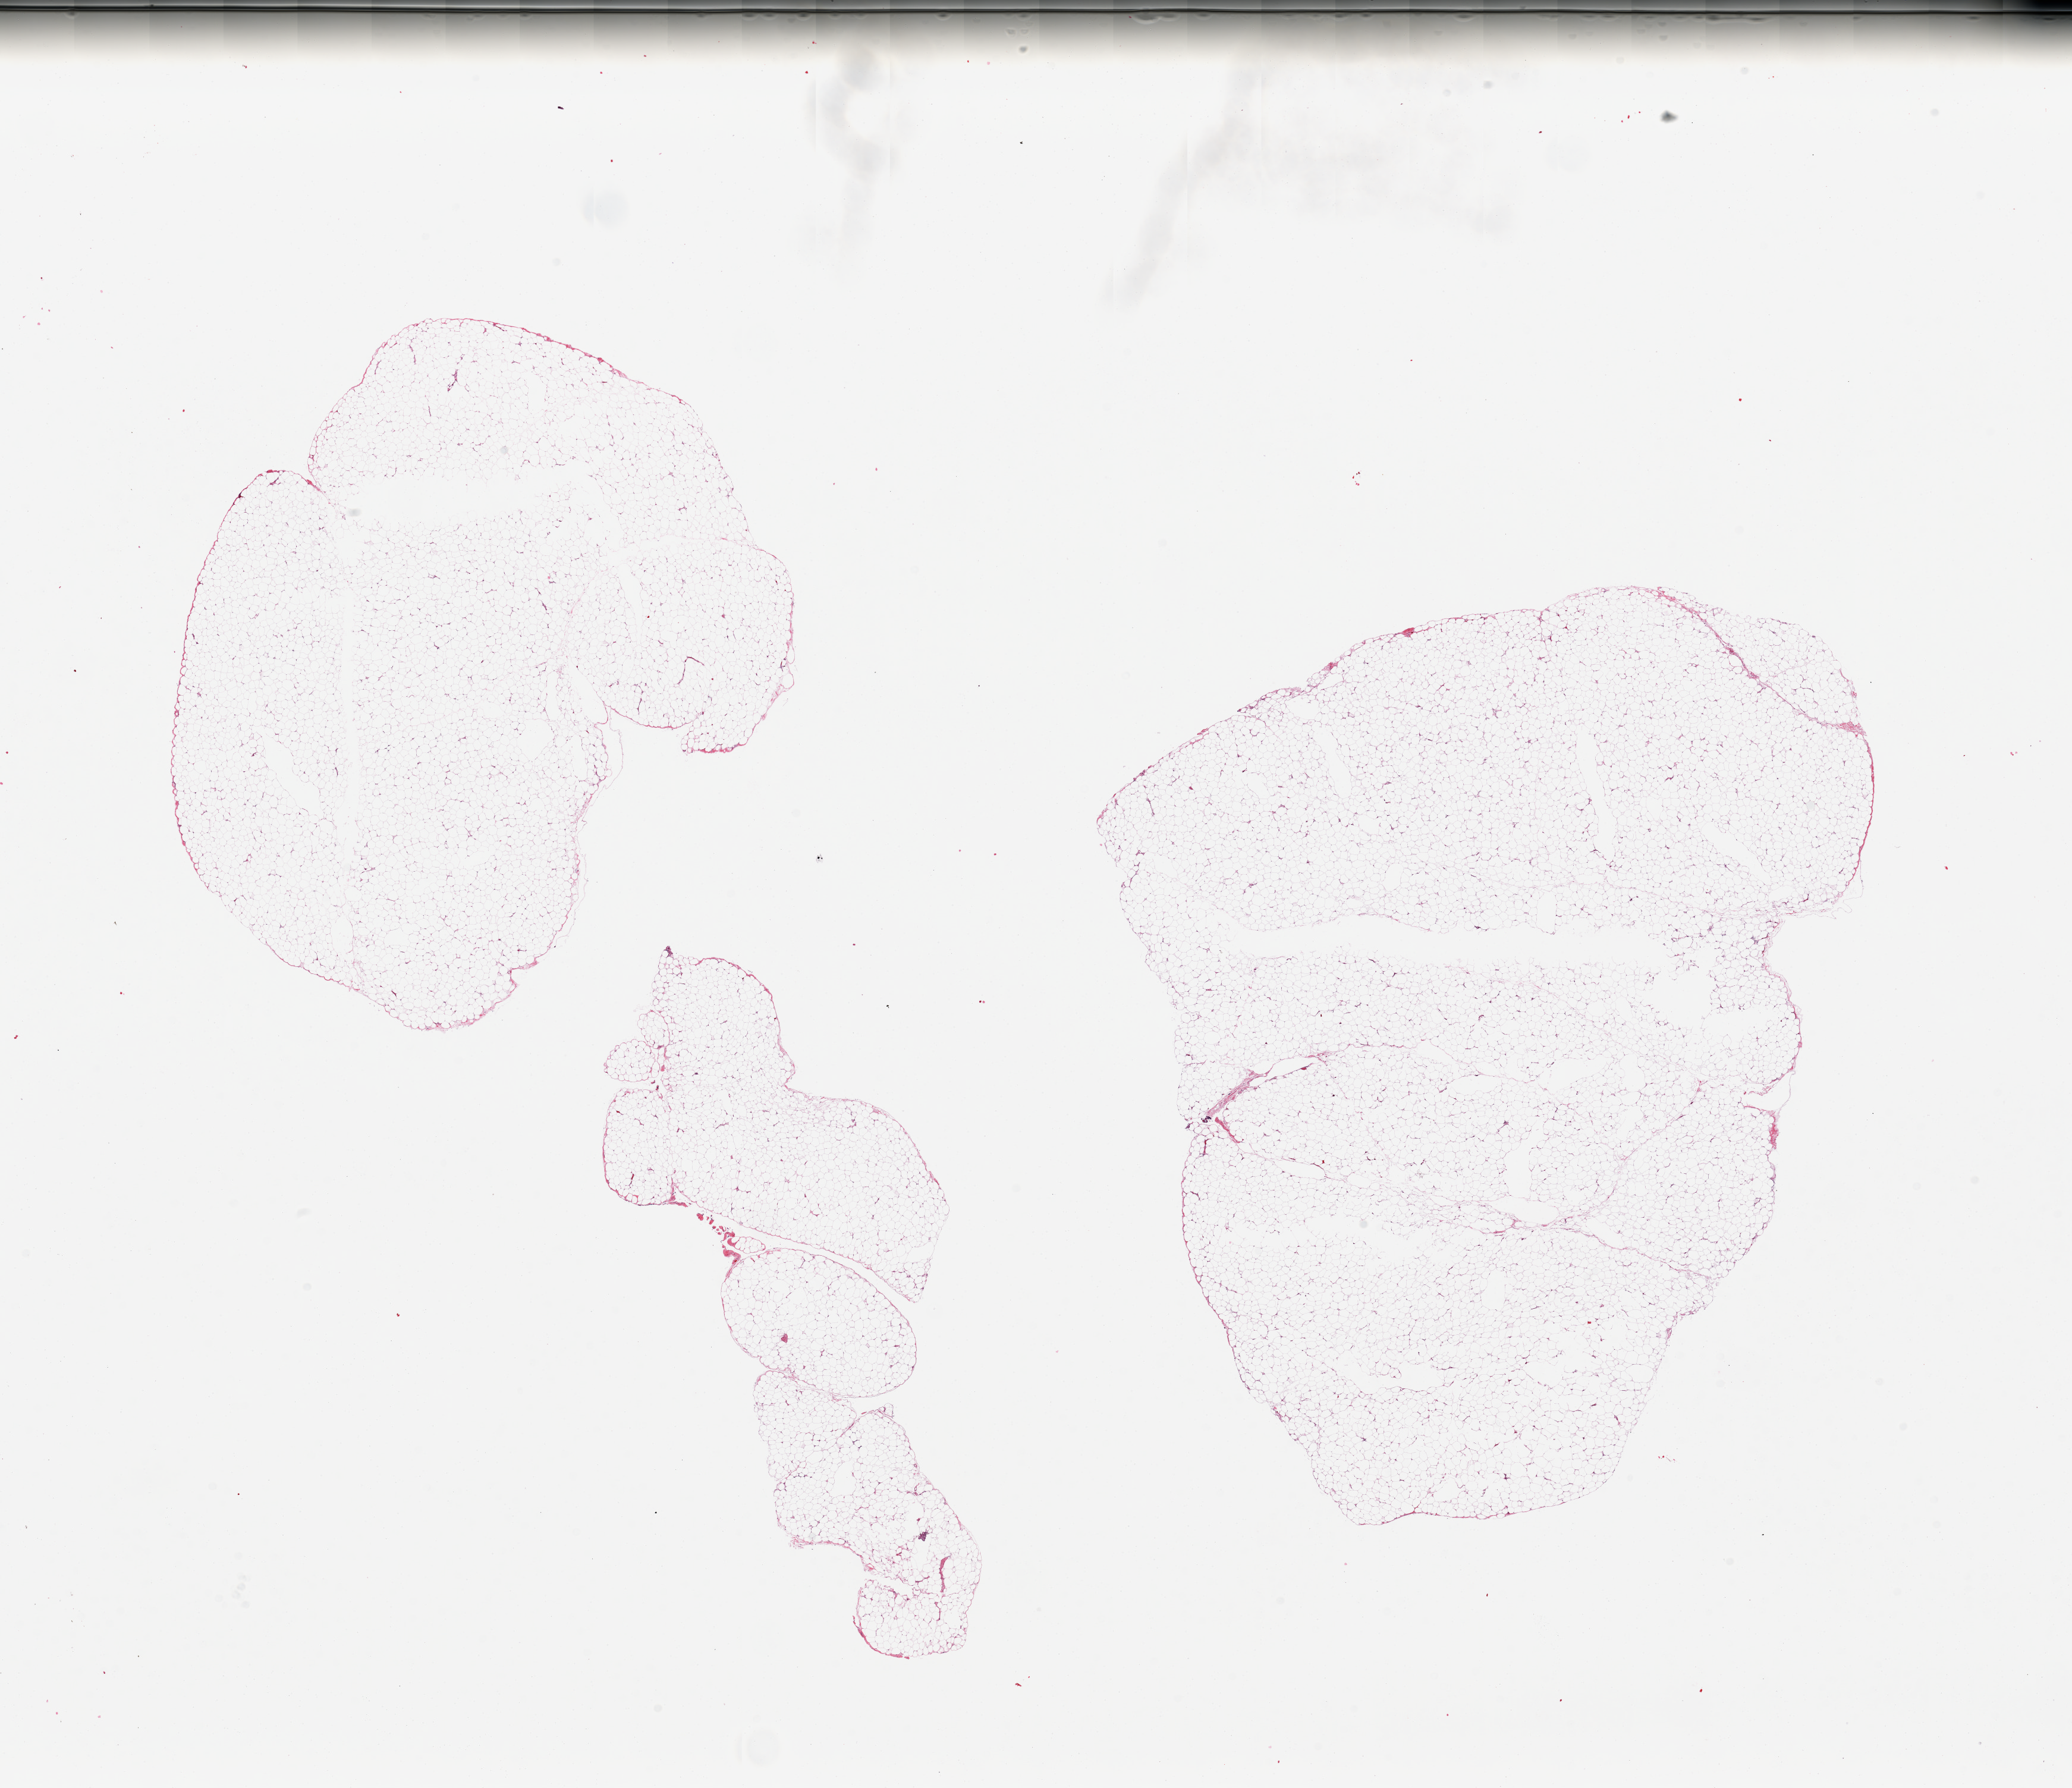
Digitized hematoxylin and eosin (H&E)-stained section, whole scanned area (about 27.6 x 23.8 mm, slide scanned at 20x) shown as a low-resolution overview; PAXgene-fixed, paraffin-embedded tissue; sampled site (target tissue): omentum; tissue donor sample. Donor sex: male.
Reviewer comment on this tissue sample: 2 pieces, pure adipose tissue, no fibrous tissue/vessels; excellent specimen.